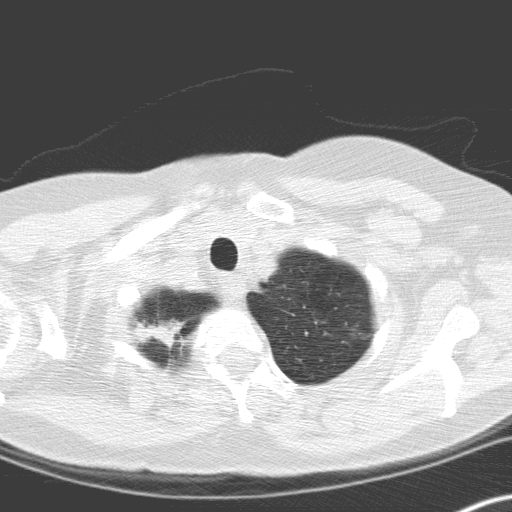
Chest CT (low-dose screening protocol), one axial image. Second screening round (one year after baseline). Lung window (W 1500 / L -600 HU). 3.2 mm slice thickness. Standard (soft-tissue) reconstruction kernel (C). 120 kVp. Slice 22 of 166 in the series. 512 × 512 image matrix. Female participant, aged 60 years at enrolment. Current smoker at enrolment.
Expert reader's lesion annotation, bounding box <126,308,197,371> (left, top, right, bottom; pixels). Reader record for this screening exam (exam-level; its link to the box is not recorded): non-calcified nodule or mass ≥4 mm, right upper lobe, 12 × 8 mm, spiculated (stellate) margins, soft tissue attenuation, pre-existing on the prior screen: no. Later outcome: lung cancer diagnosed 58 days after this screen — squamous cell carcinoma, keratinizing, NOS, right upper lobe, moderately differentiated (G2), stage IA (AJCC 6th edition), 20 mm at pathology.